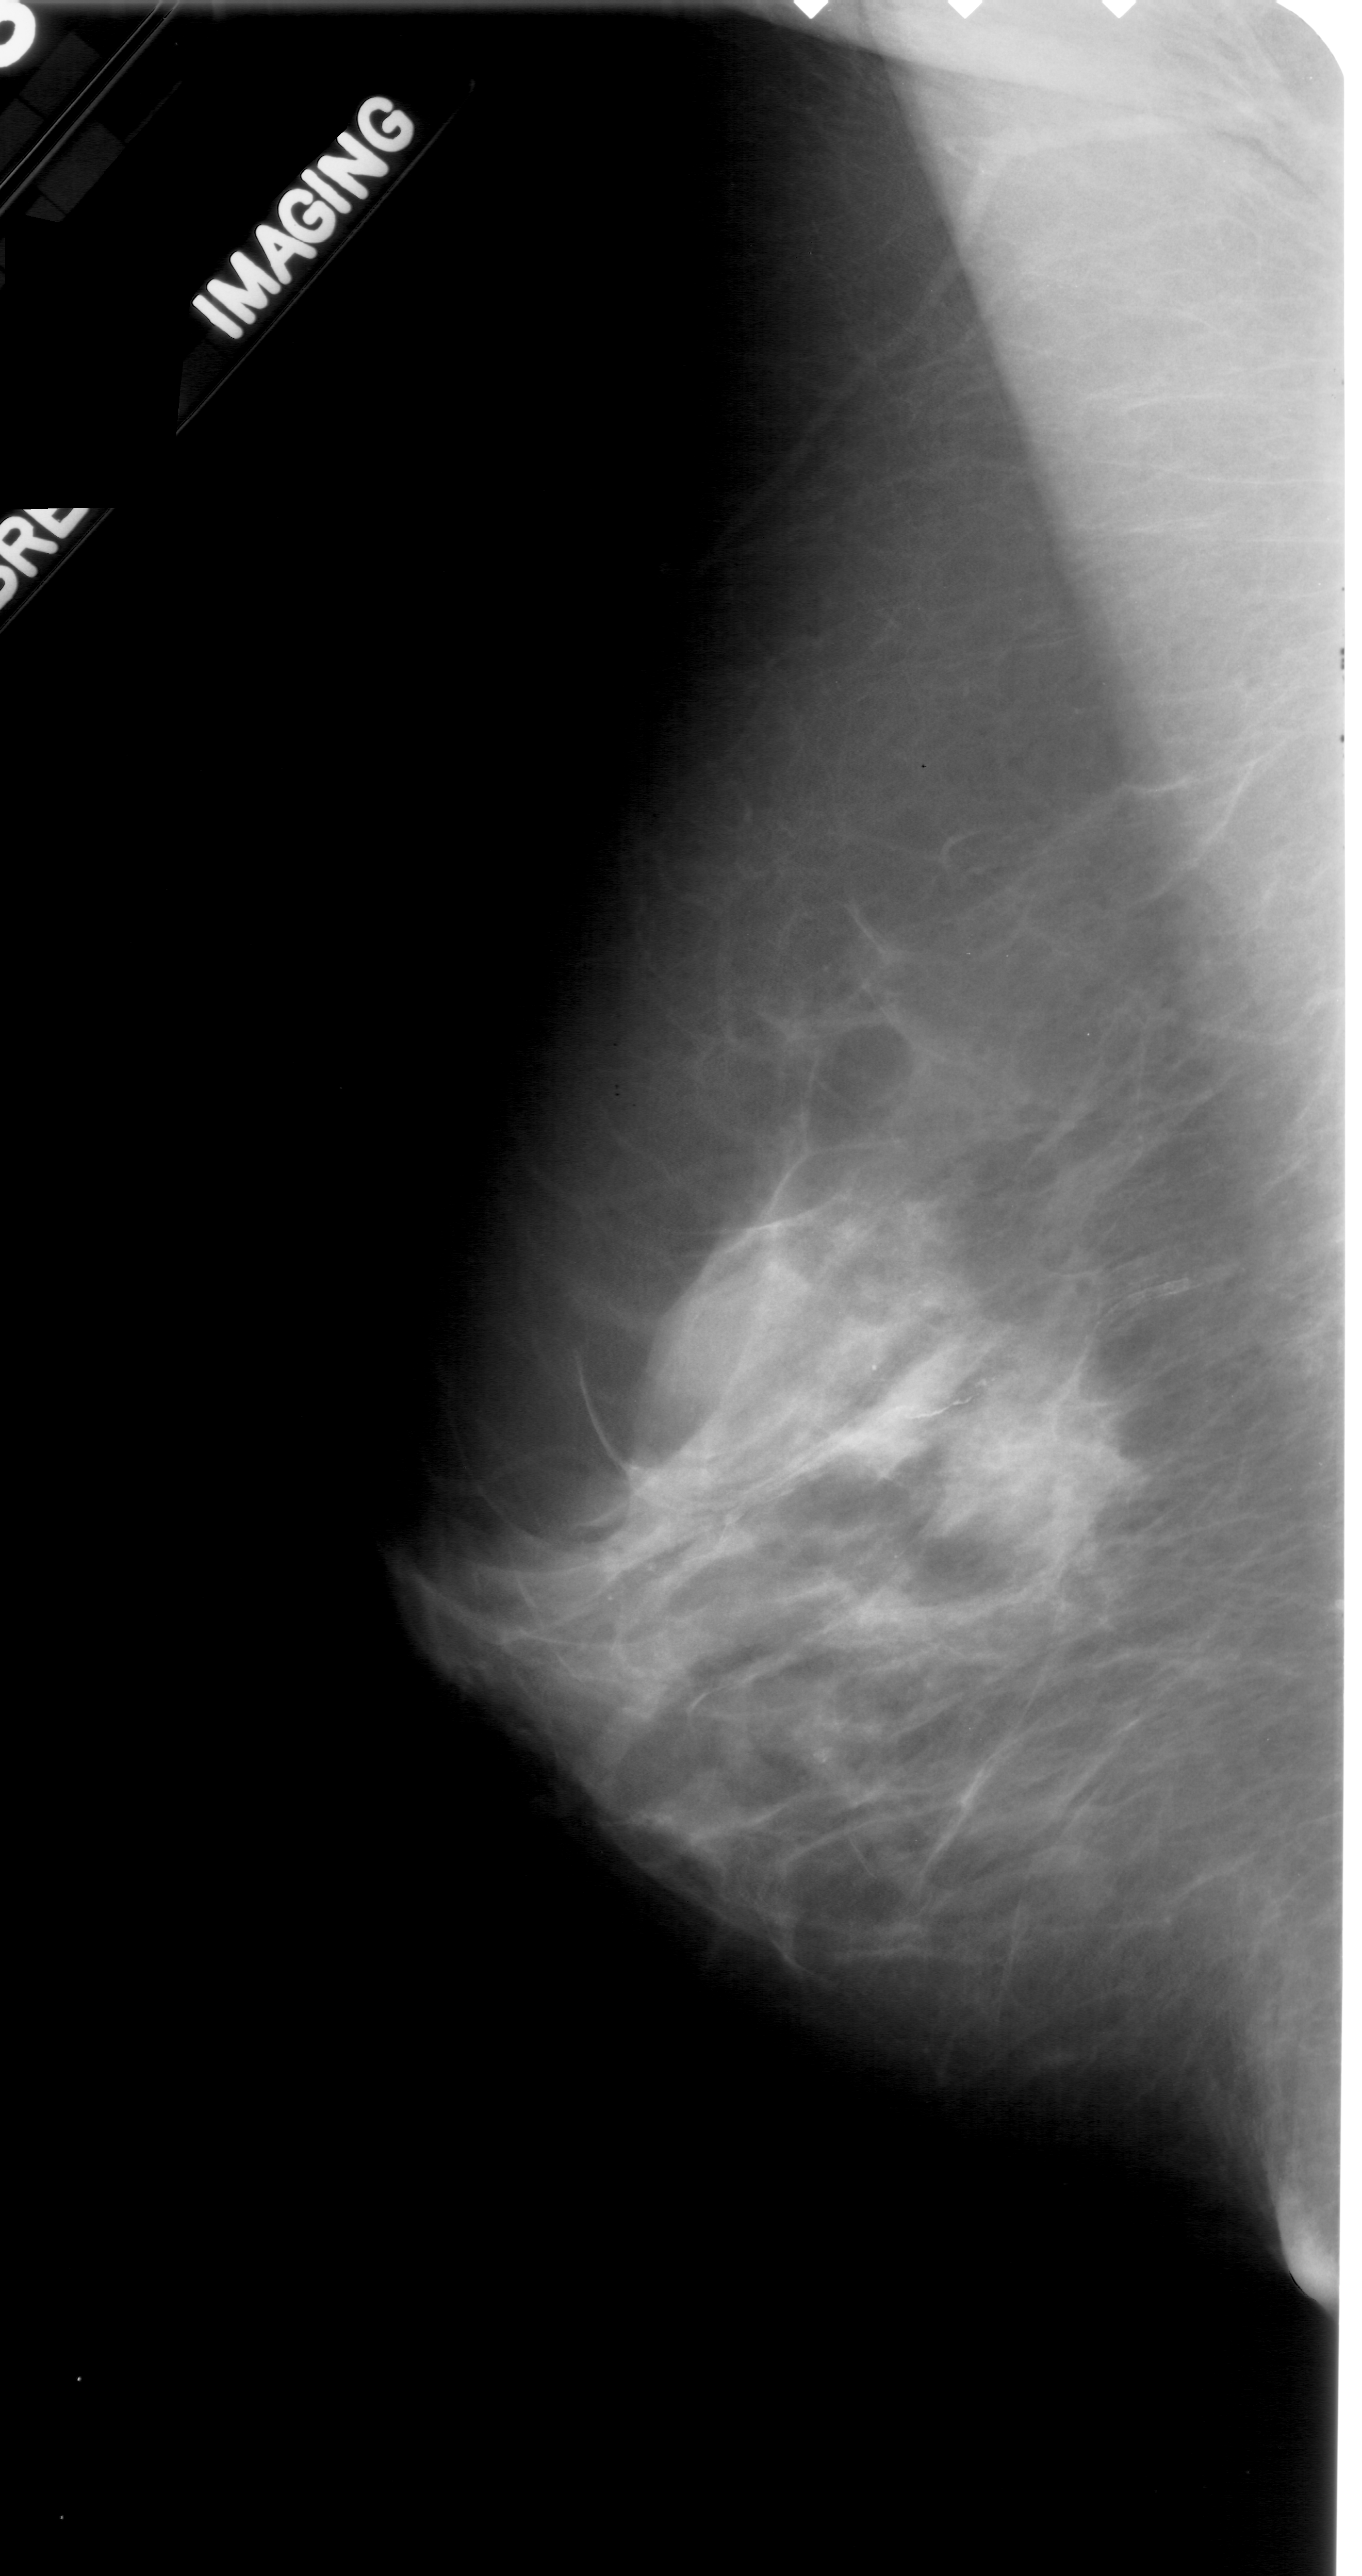
Scanned film-screen mammogram, left breast, MLO view, BI-RADS breast density category 2 (scale 1–4).
- Marked abnormality: mass, shape oval, margins ill defined; BI-RADS assessment category 4; subtlety rating 4 on a 1 (subtle) to 5 (obvious) scale; pathology result (as recorded, not read from the image): malignant.